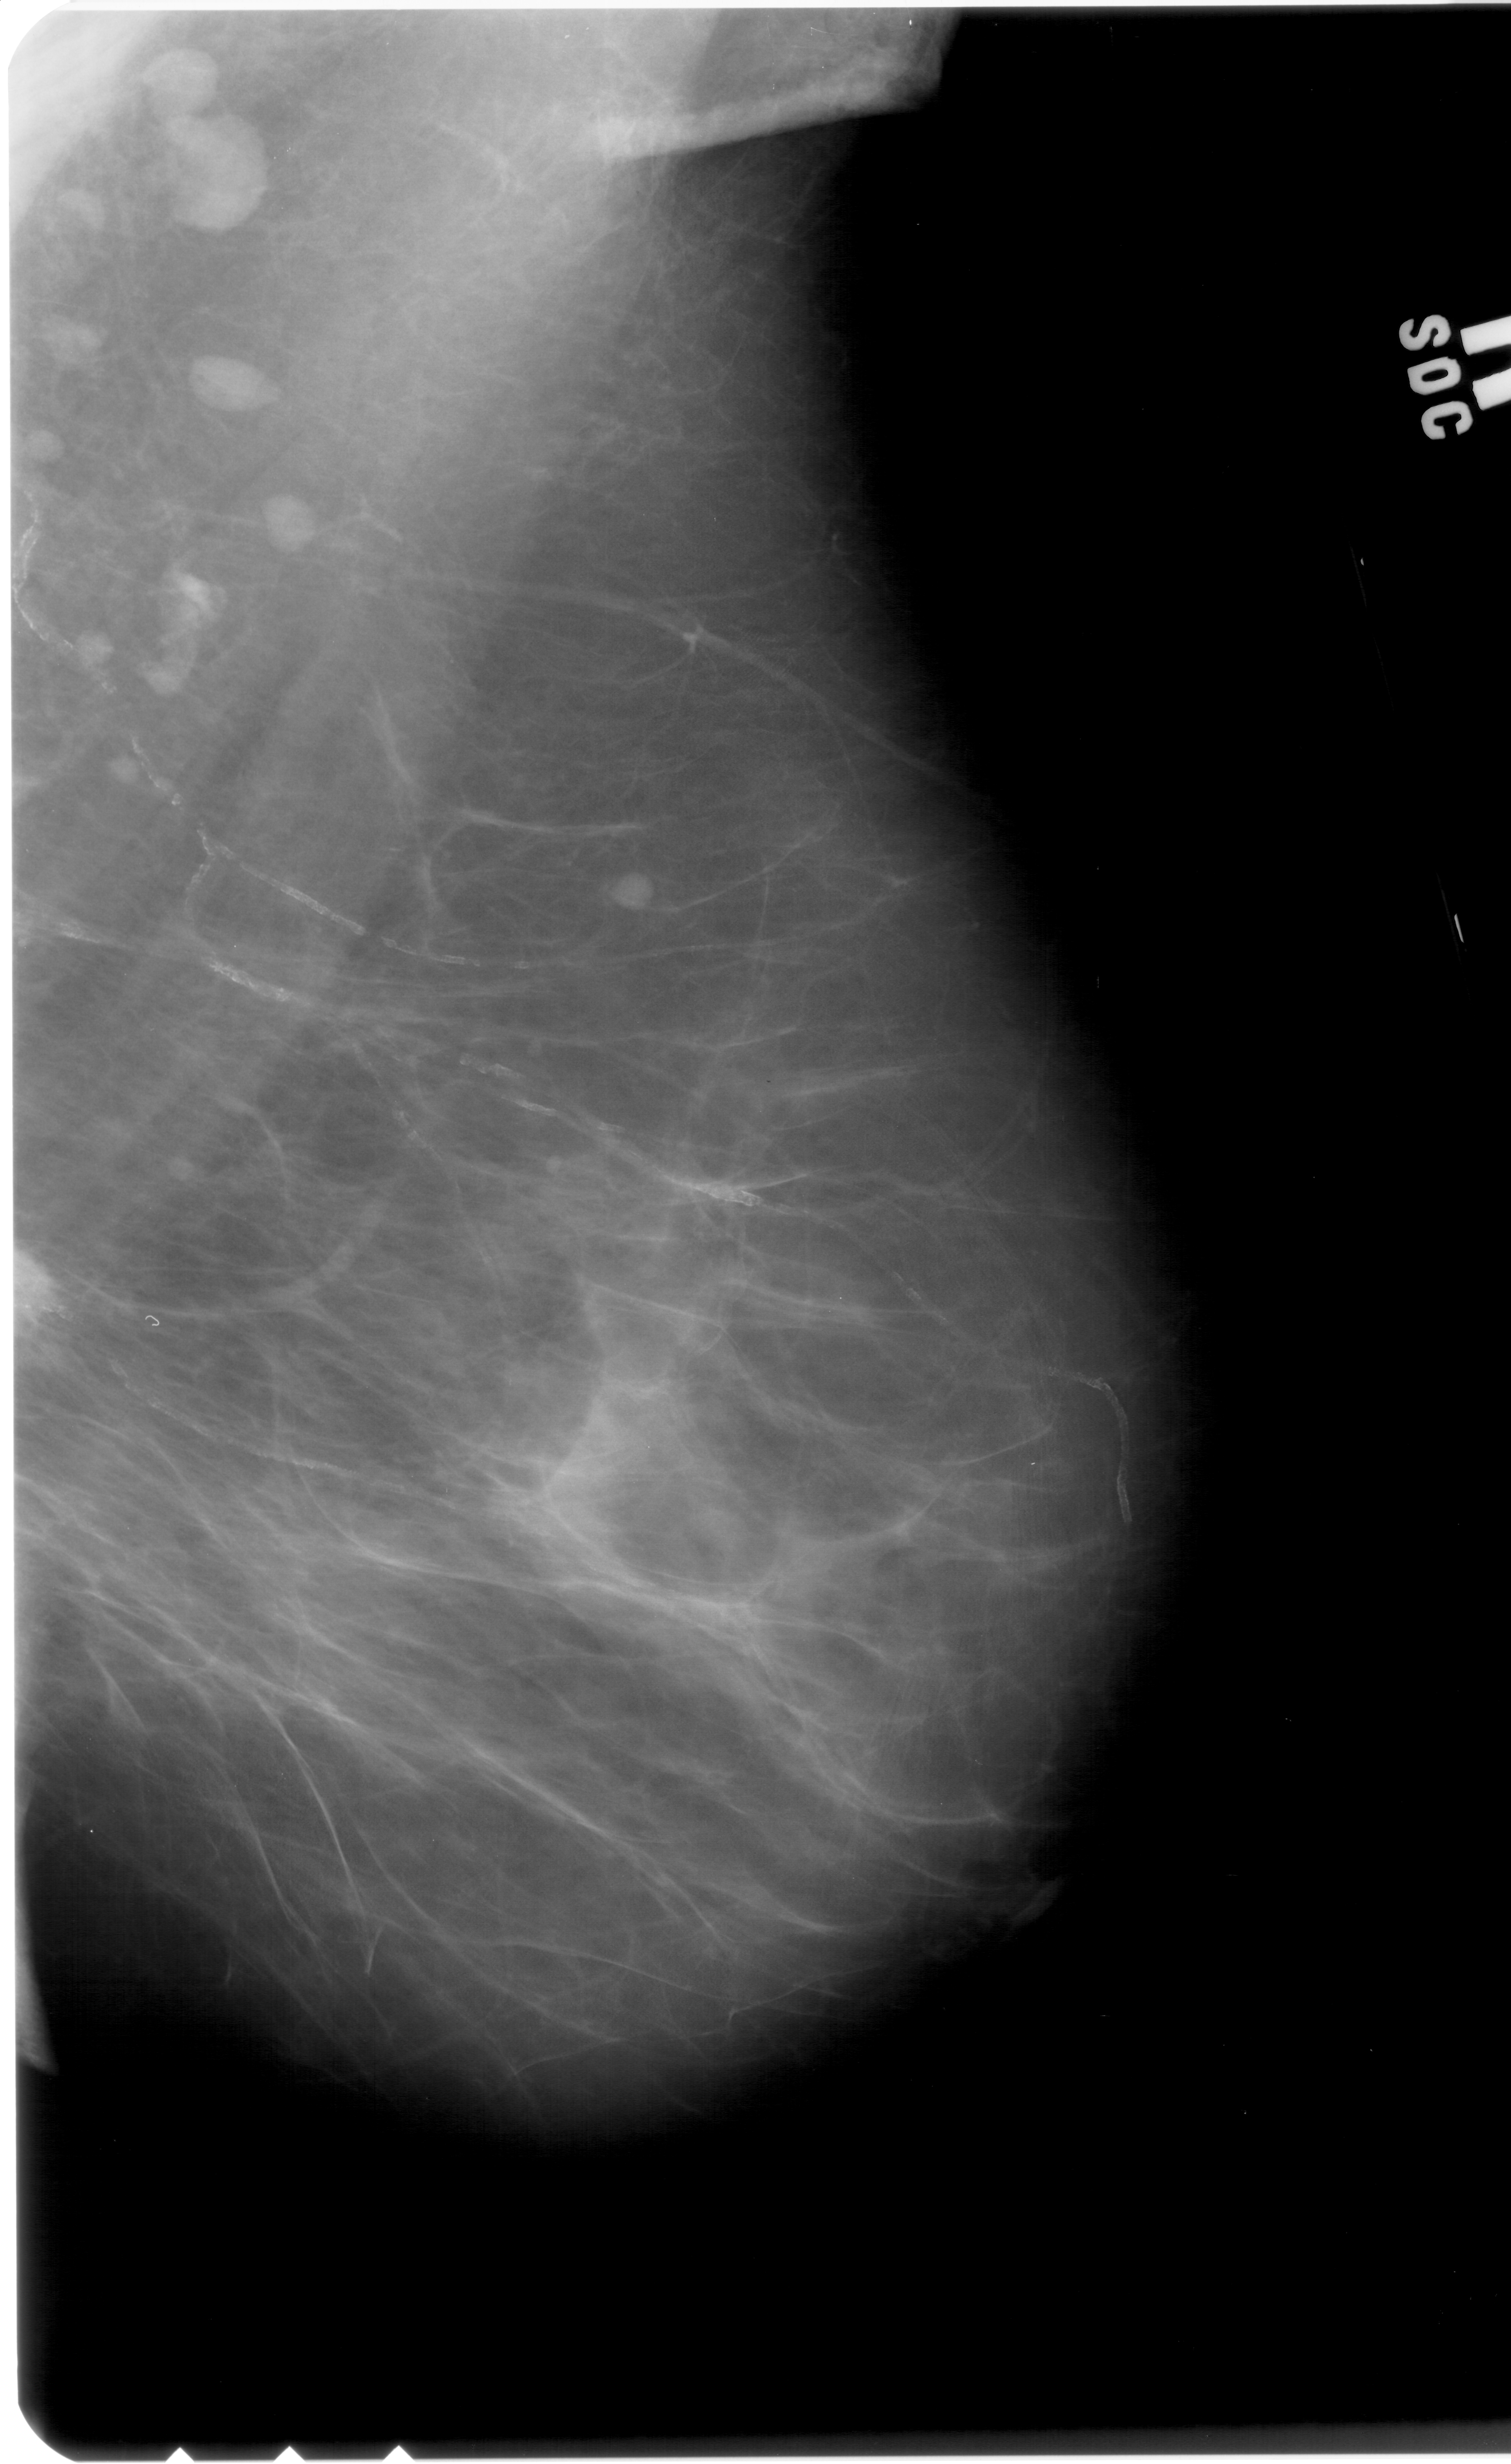
Digitized screen-film mammogram; right breast; MLO view; BI-RADS breast density category 4 (scale 1–4).
Radiologist-marked abnormalities on this image: mass, shape irregular, margins ill defined; BI-RADS assessment category 4; pathology (as recorded): malignant.